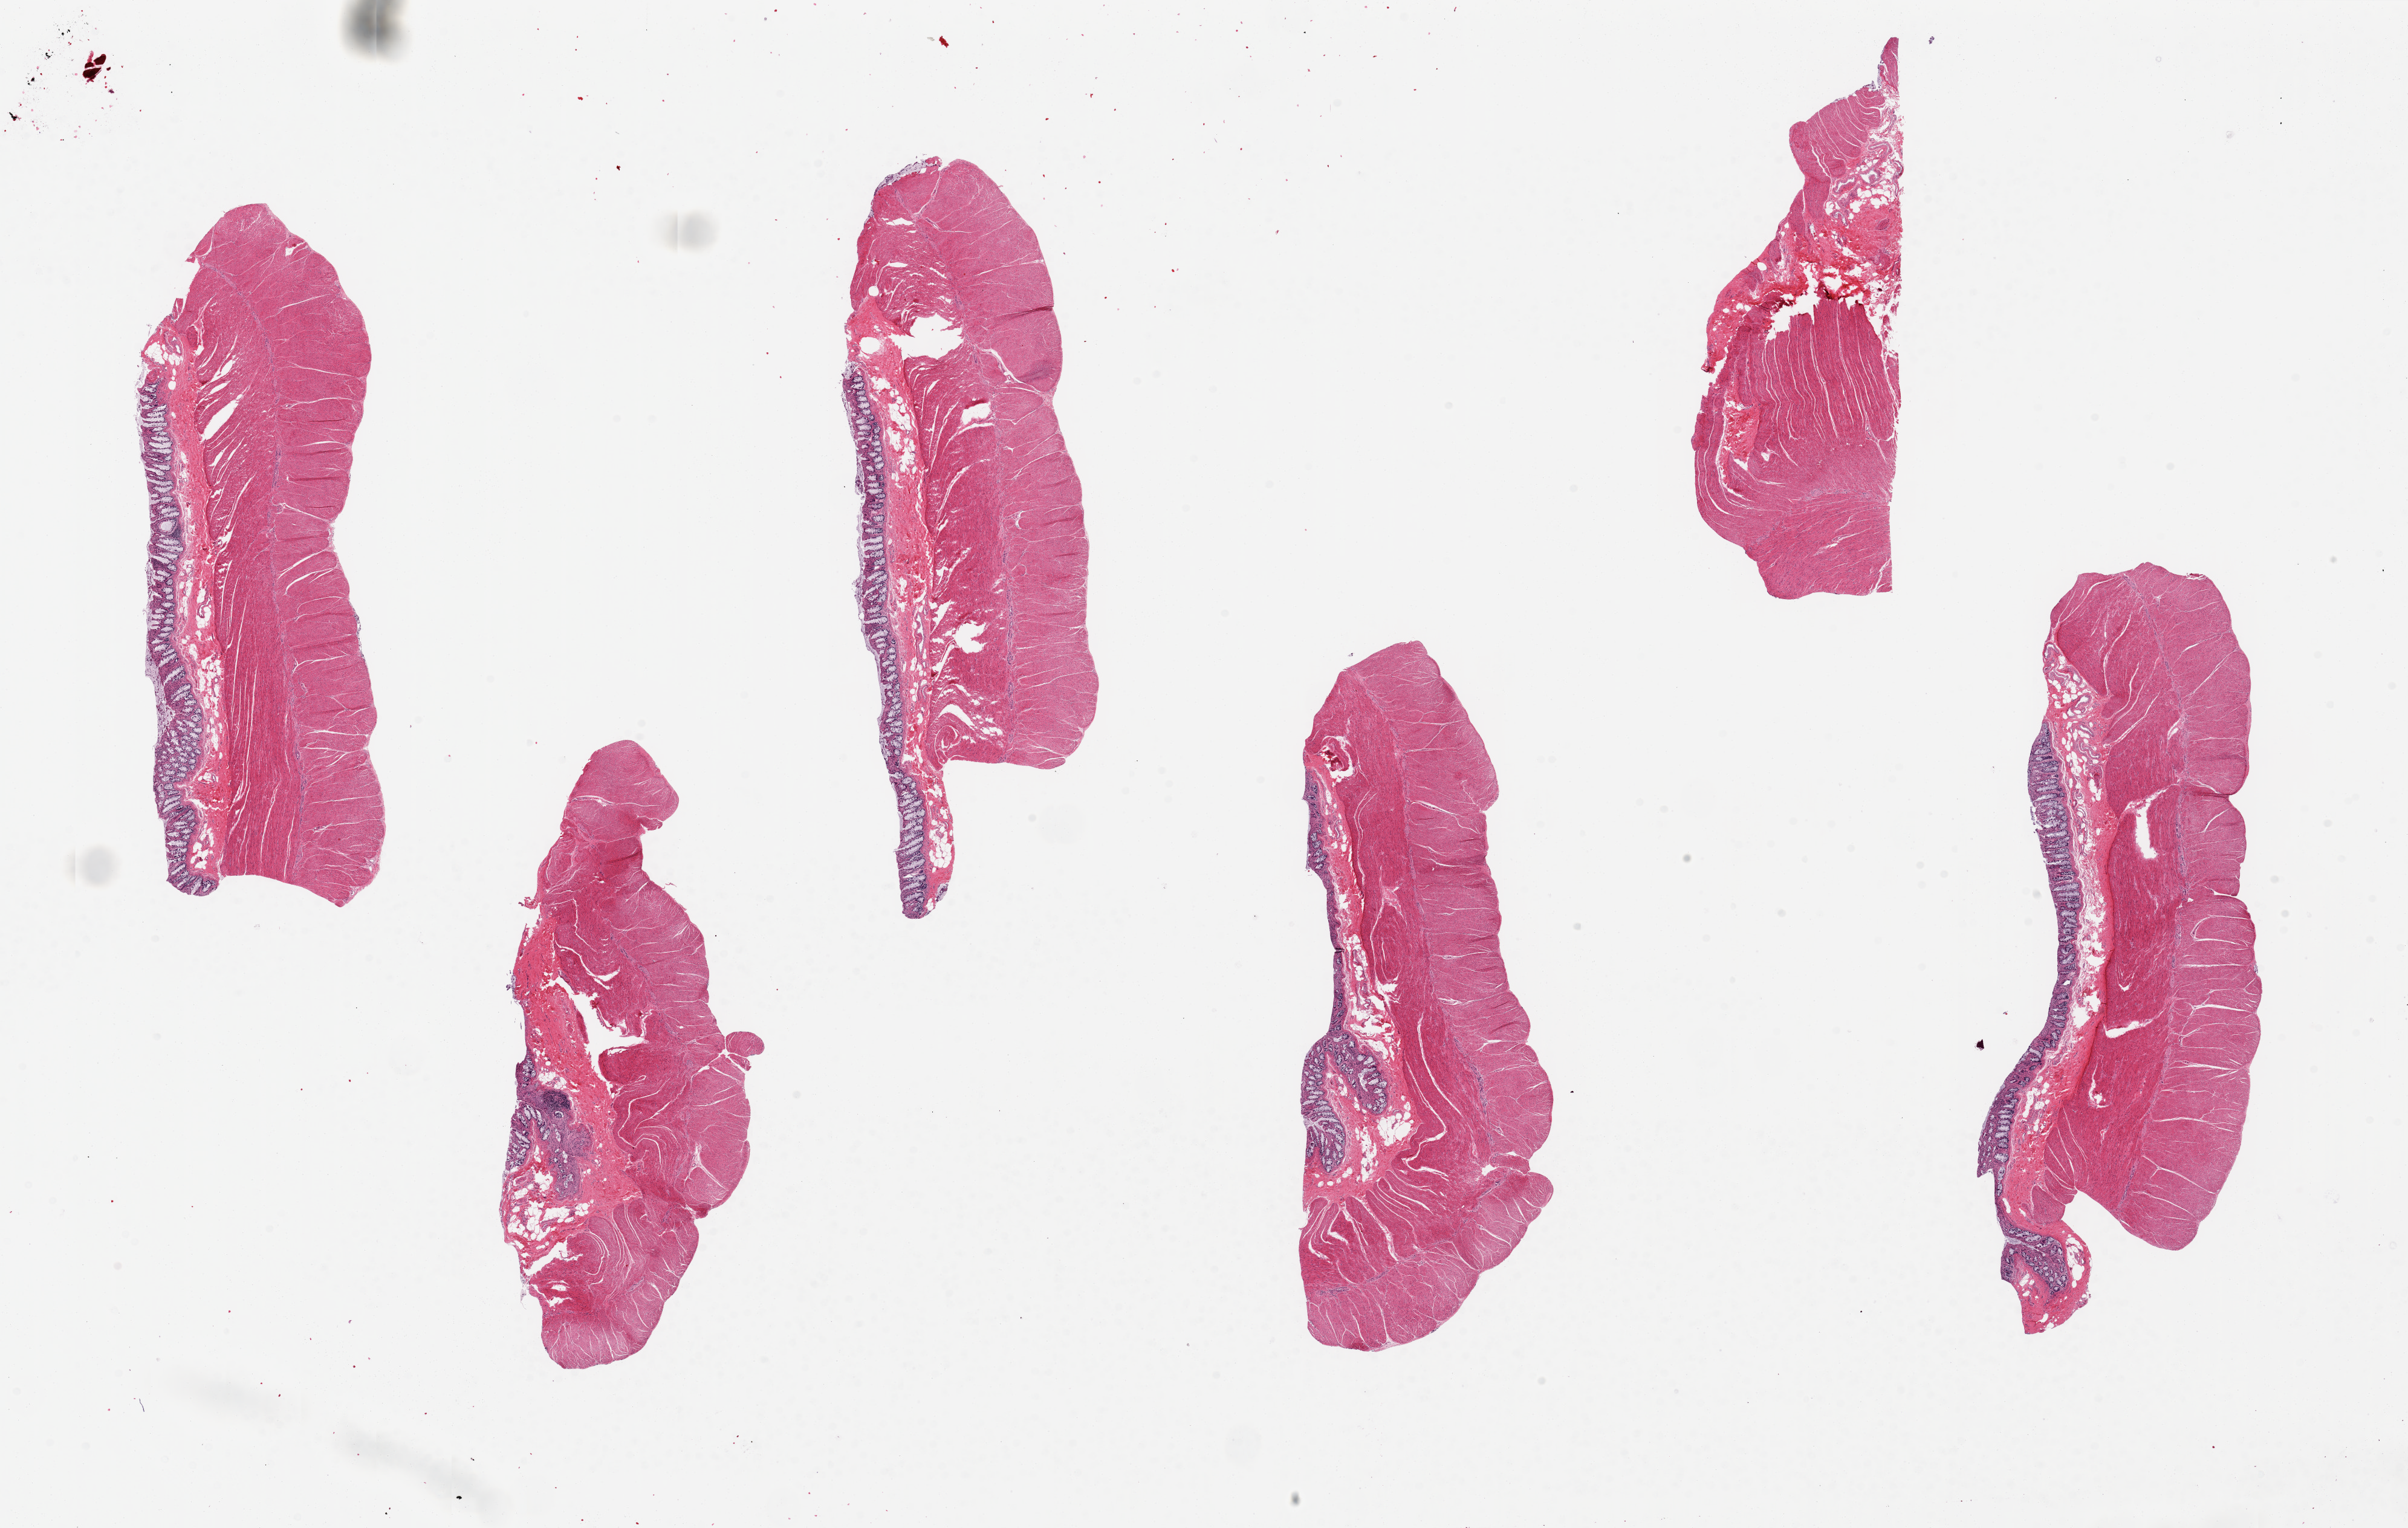
Digitized haematoxylin and eosin-stained section, brightfield, a low-resolution overview of the entire scanned area, about 31.5 x 20.0 mm. PAXgene-fixed paraffin-embedded (PFPE) section. Sampled site (target tissue): sigmoid colon. Donor tissue sample. Donor: male.
- pathologist's review note for this sample: 6 pieces, up to 10x4mm; mainly muscularis: <10% total tissue is mucosa